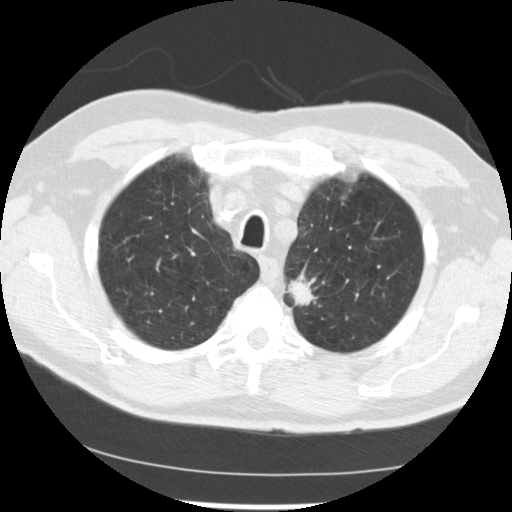
Low-dose screening chest CT, one axial slice; position 202 of 249 along the scan axis; reconstruction kernel STANDARD; 120 kVp; lung window (W 1500 / L -600 HU); 2.5 mm slice thickness; 512 × 512 image matrix, field of view 341 × 341 mm.
Annotated regions visible in this slice (expert manual segmentation):
- lesion 2 (tumor, upper lobe of left lung): bounding box [x1, y1, x2, y2] px = [289, 278, 316, 306]